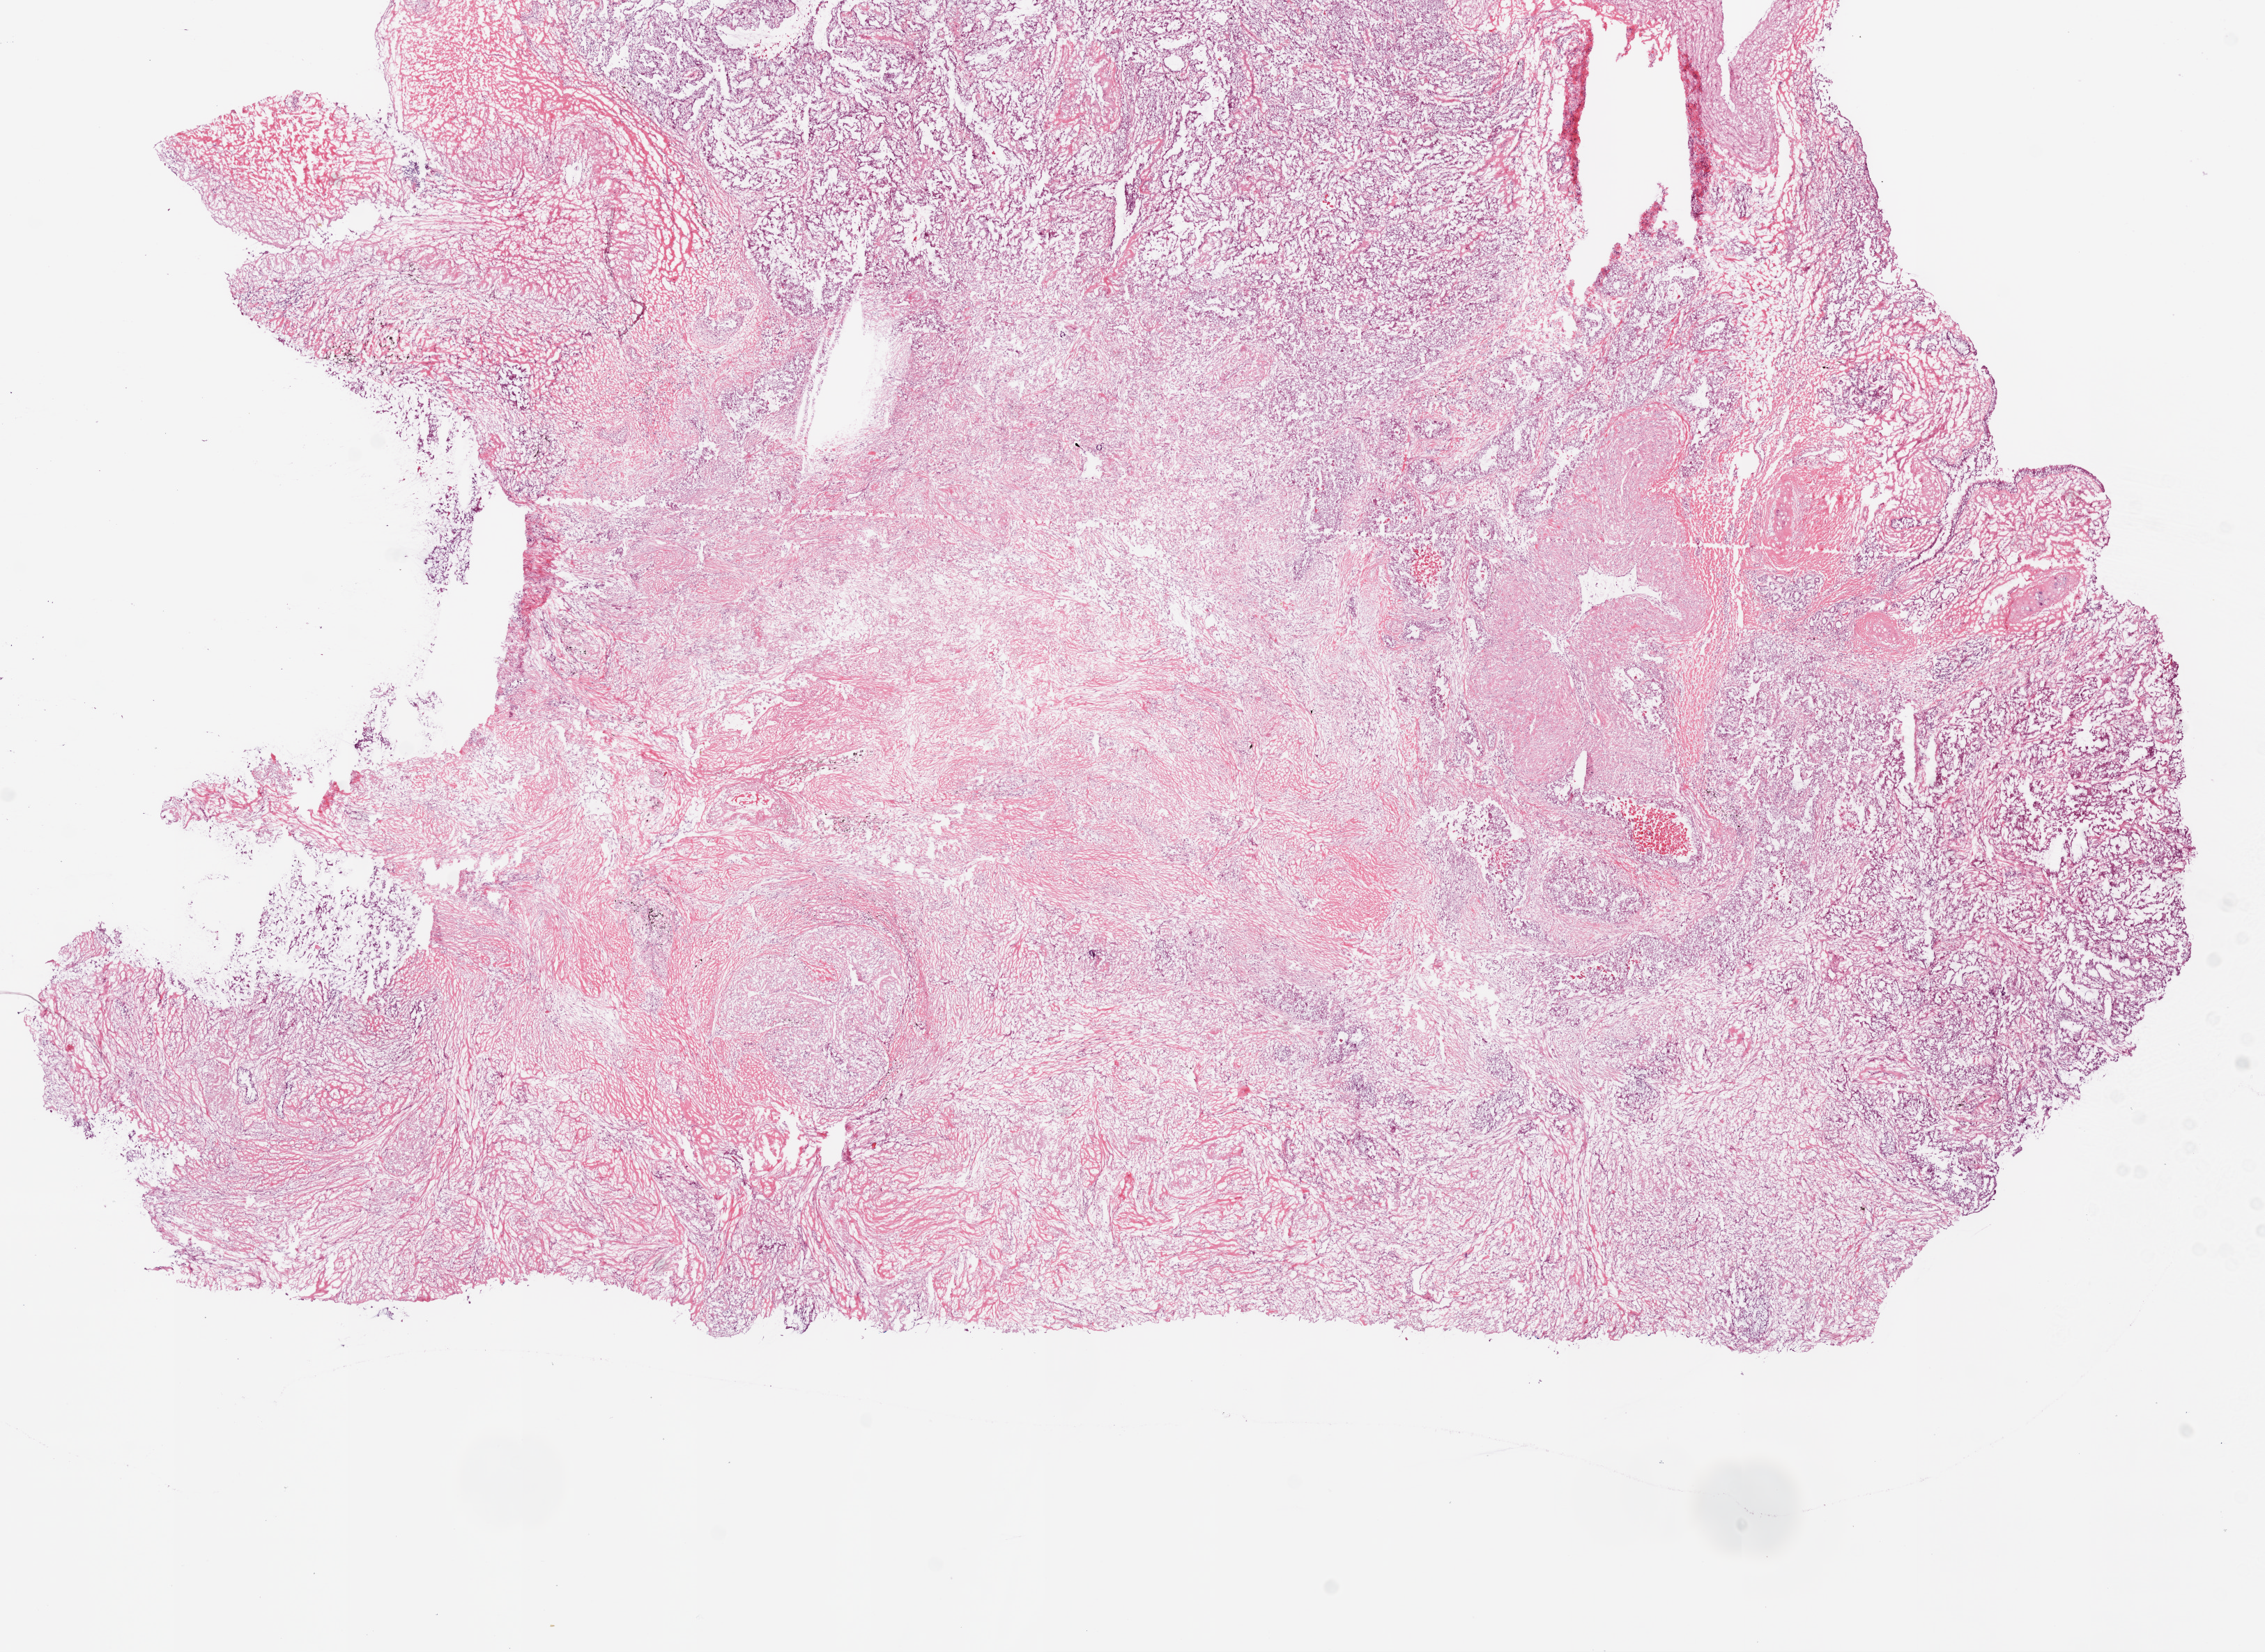
H&E-stained whole-slide image, shown as a low-resolution overview of the whole scanned area (about 13.0 x 9.5 mm); frozen section; sample: primary tumour, lung. Female patient; age at initial diagnosis 64 years.
Histologic diagnosis: Adenocarcinoma, NOS (upper lobe, lung).